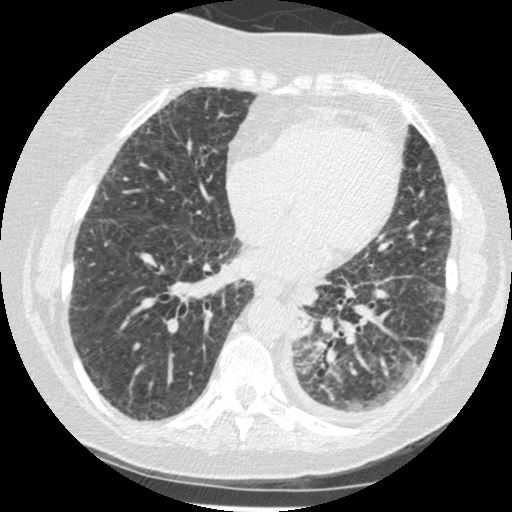
Low-dose screening chest CT, one axial slice; reconstruction kernel STANDARD; lung window (W 1500 / L -600 HU); 1.25 mm slice thickness; 512 × 512 image matrix, field of view 310 × 310 mm.
Outlined on this slice (manually delineated by an expert):
- lesion 1 (tumor, lower lobe of left lung): bounding box [x1, y1, x2, y2] px = [294, 323, 313, 337]